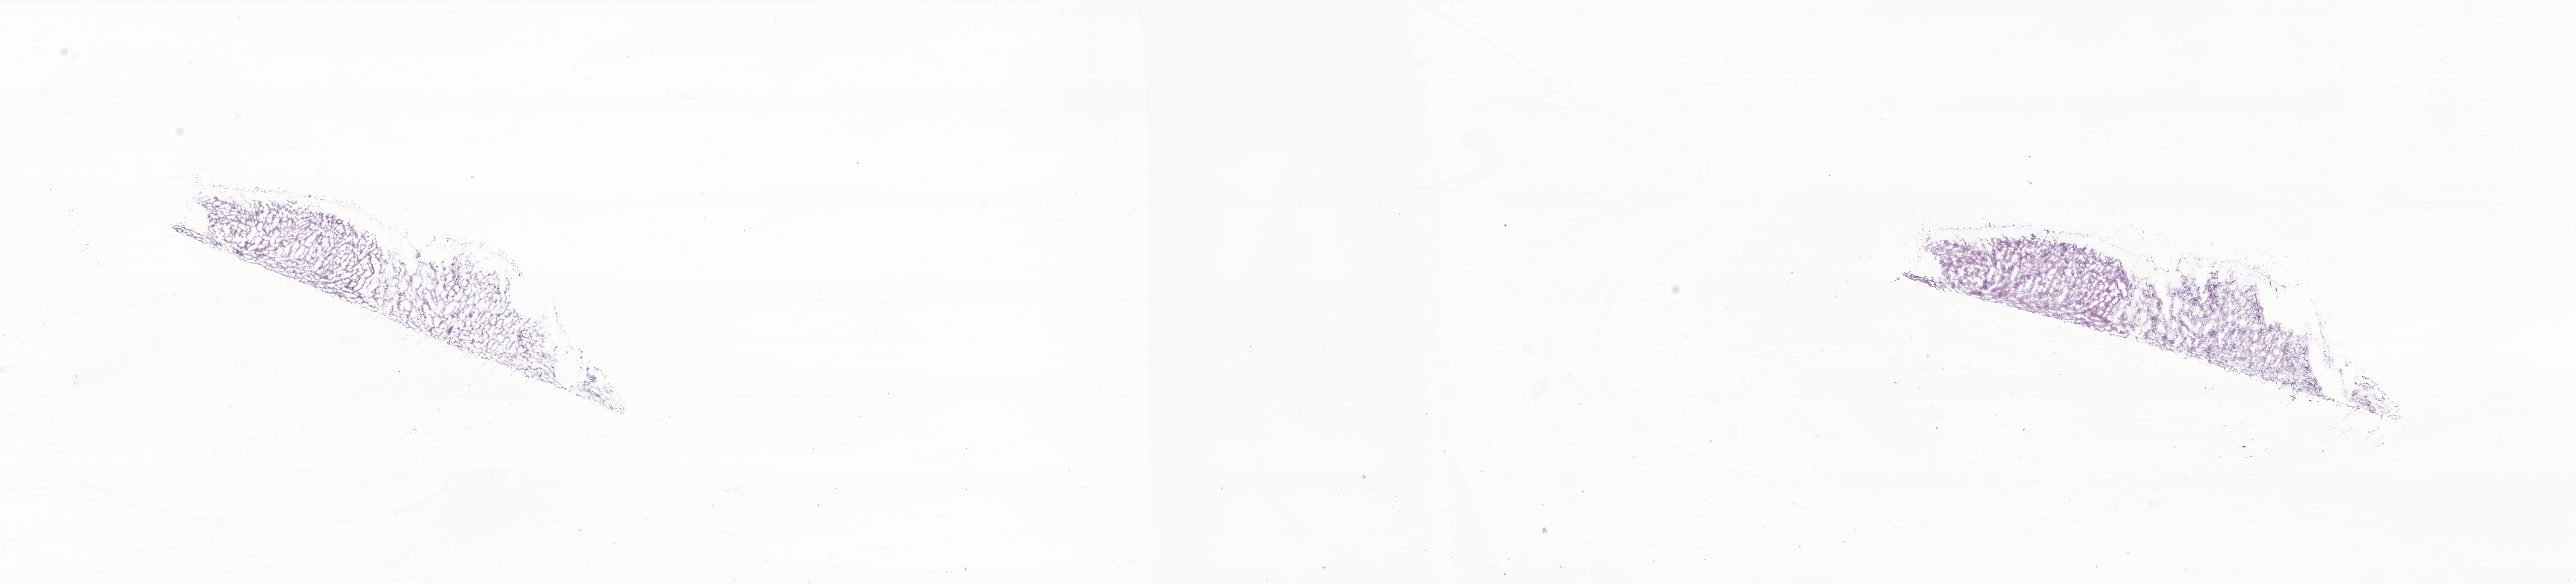
Digitized haematoxylin and eosin-stained section of tumor tissue from the brain — a low-resolution overview of the entire scanned area, about 28.9 x 6.6 mm, frozen section (OCT-embedded). Female patient, age 76 months (6 years 4 months).
Recorded diagnosis: Neoplasm, uncertain whether benign or malignant.